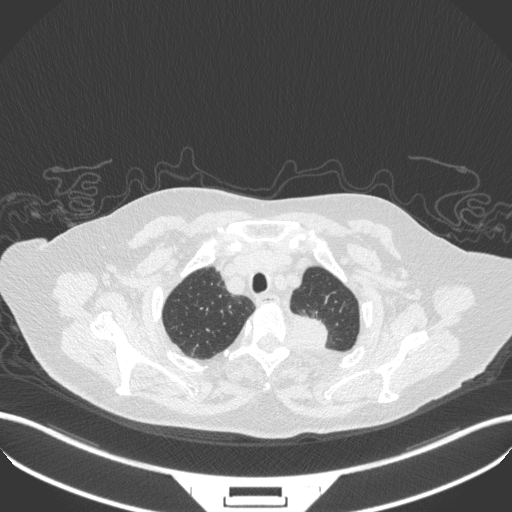
Chest CT, one axial slice. Position 301 of 353 along the scan axis. Reconstruction kernel B31f. Lung window (W 1500 / L -600 HU). 1 mm slice thickness. 512 × 512 image matrix. Female patient, age 81 years. Case-level facts recorded for this patient, not image findings: clinical TNM (as recorded): T2a N0 M0.
Structures marked on this image (bounding box drawn by a radiologist):
- lung tumour (recorded histology: adenocarcinoma): bounding box (x1, y1, x2, y2) in pixels: (289, 312, 336, 356)